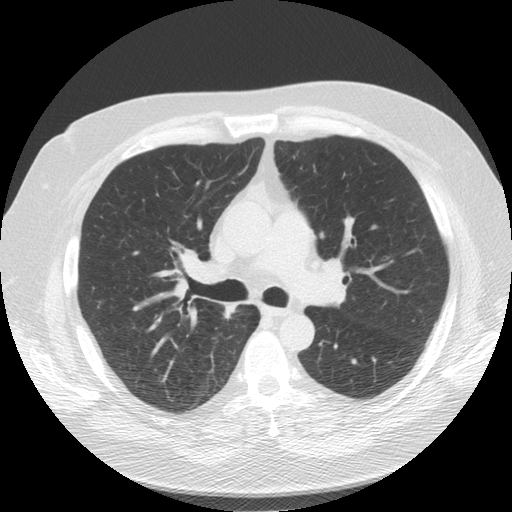
Low-dose screening chest CT, one axial slice. Position 90 of 136 along the scan axis. Lung window (W 1500 / L -600 HU). 2.5 mm slice thickness. 512 × 512 image matrix, field of view 360 × 360 mm.
Outlined on this slice (manually delineated by an expert):
- lesion 1 (tumor, upper lobe of right lung): bounding box (x1, y1, x2, y2) in pixels: (225, 304, 236, 318)